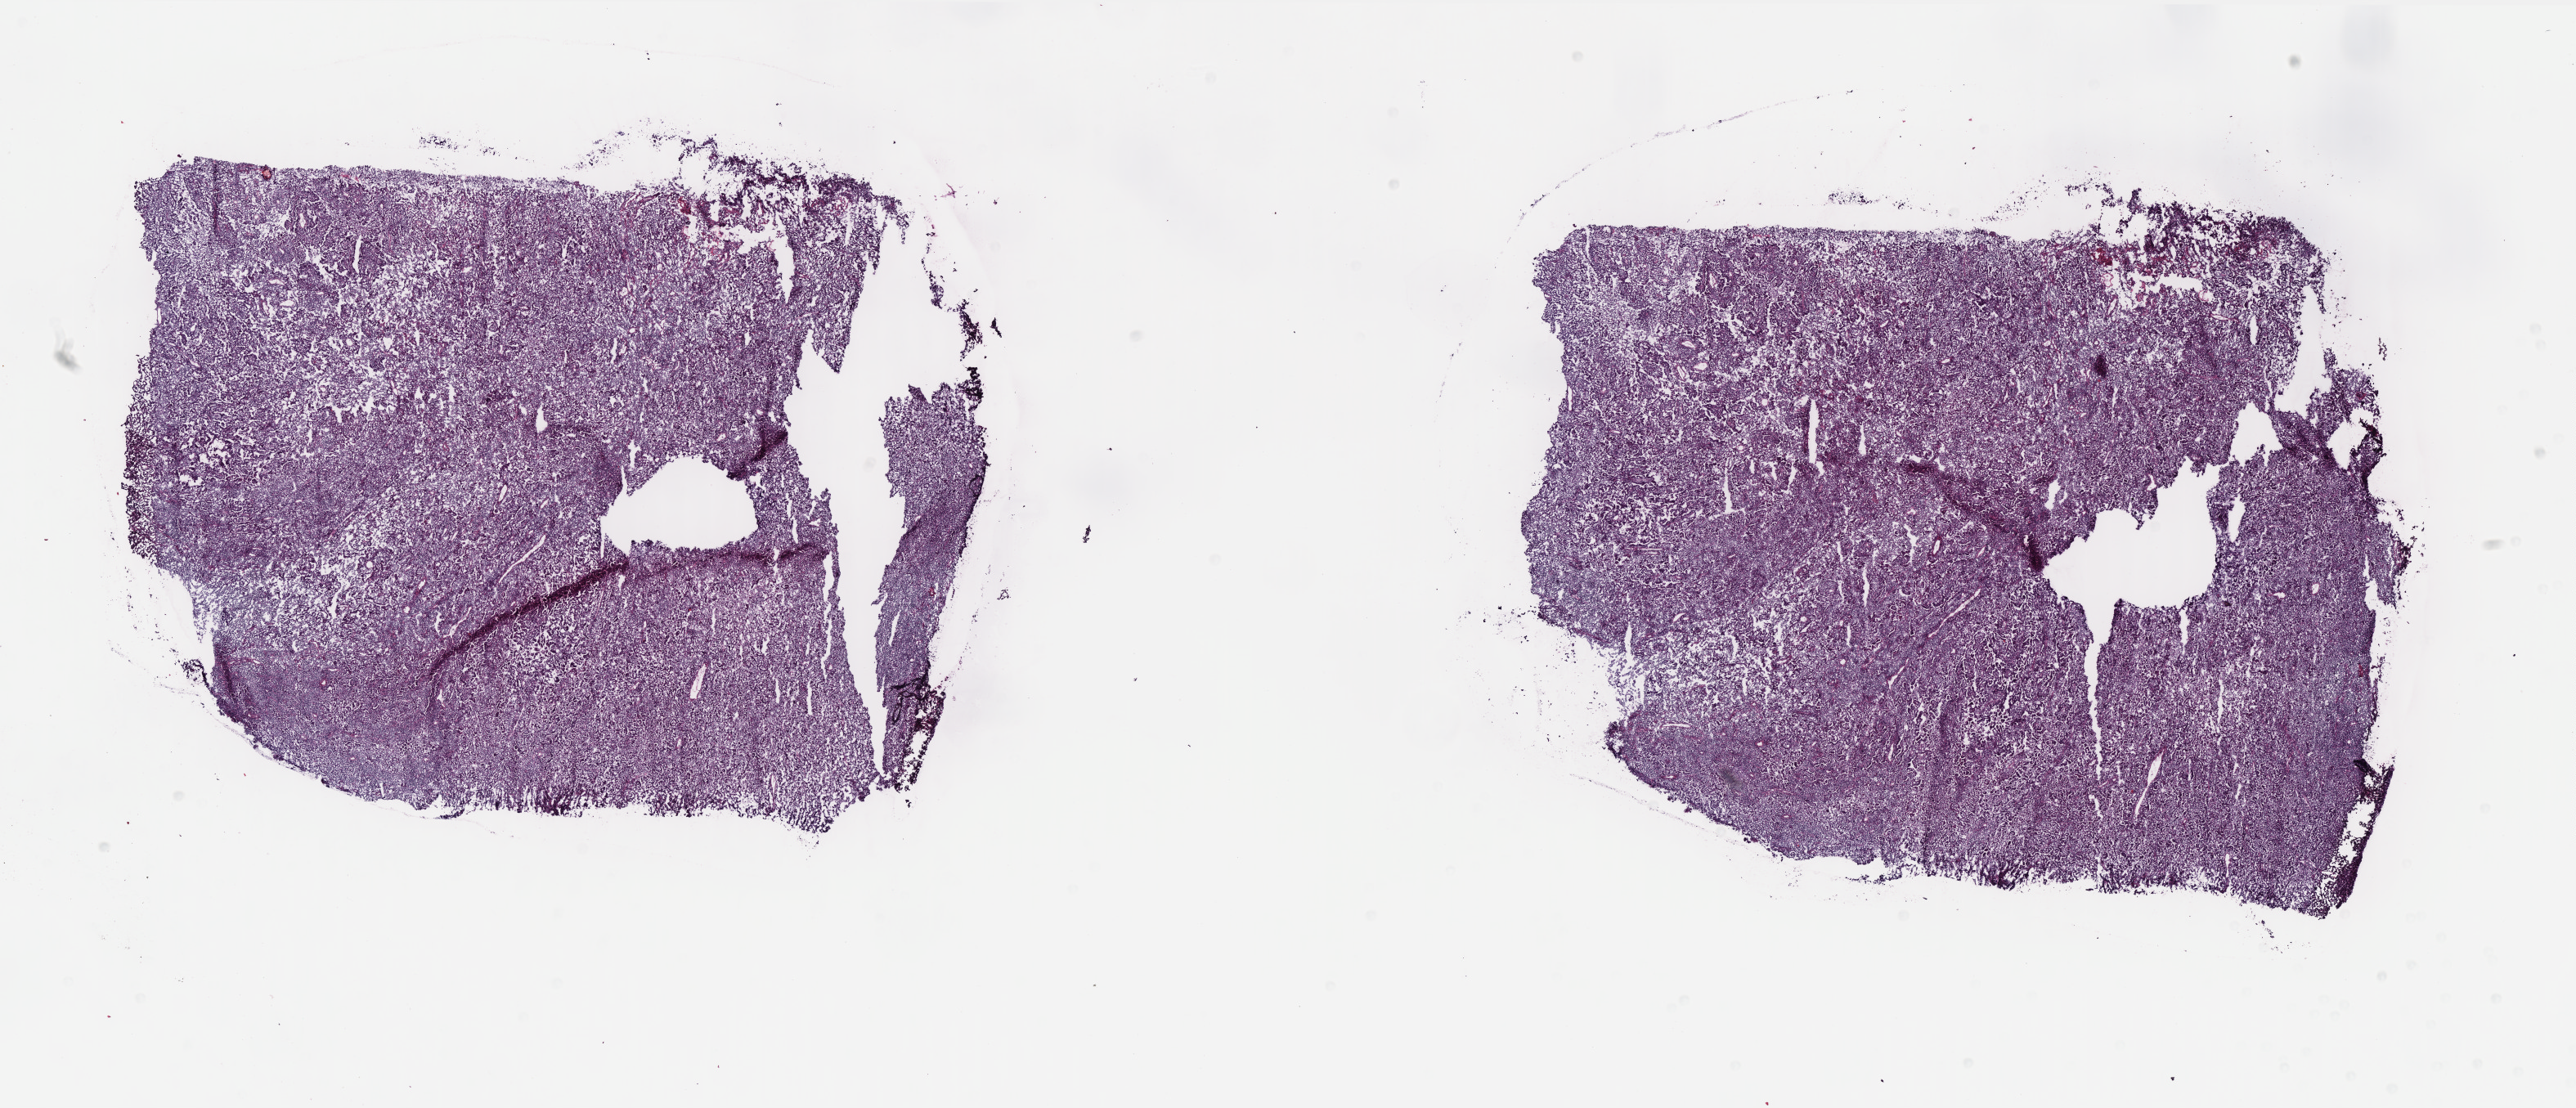
Whole-slide histology image, H&E-stained, whole scanned area (about 25.3 x 10.9 mm) shown as a low-resolution overview, frozen section from the top of the tissue portion, uterus, primary tumour sample. Female patient; age at initial diagnosis 67 years. Histologic grade: G3 (poorly differentiated). Pathologist review of this section (percent, as recorded): tumour cells 60%, tumour nuclei 60%, normal cells 10%, stromal cells 25%, necrosis 5%. Infiltration values recorded for this section: lymphocyte infiltration 90%, monocyte infiltration 0%, neutrophil infiltration 0%.
FIGO stage: IA. Histologic diagnosis: Serous cystadenocarcinoma, NOS (endometrium). Lymph nodes positive (case pathology): 0 of 10 examined.